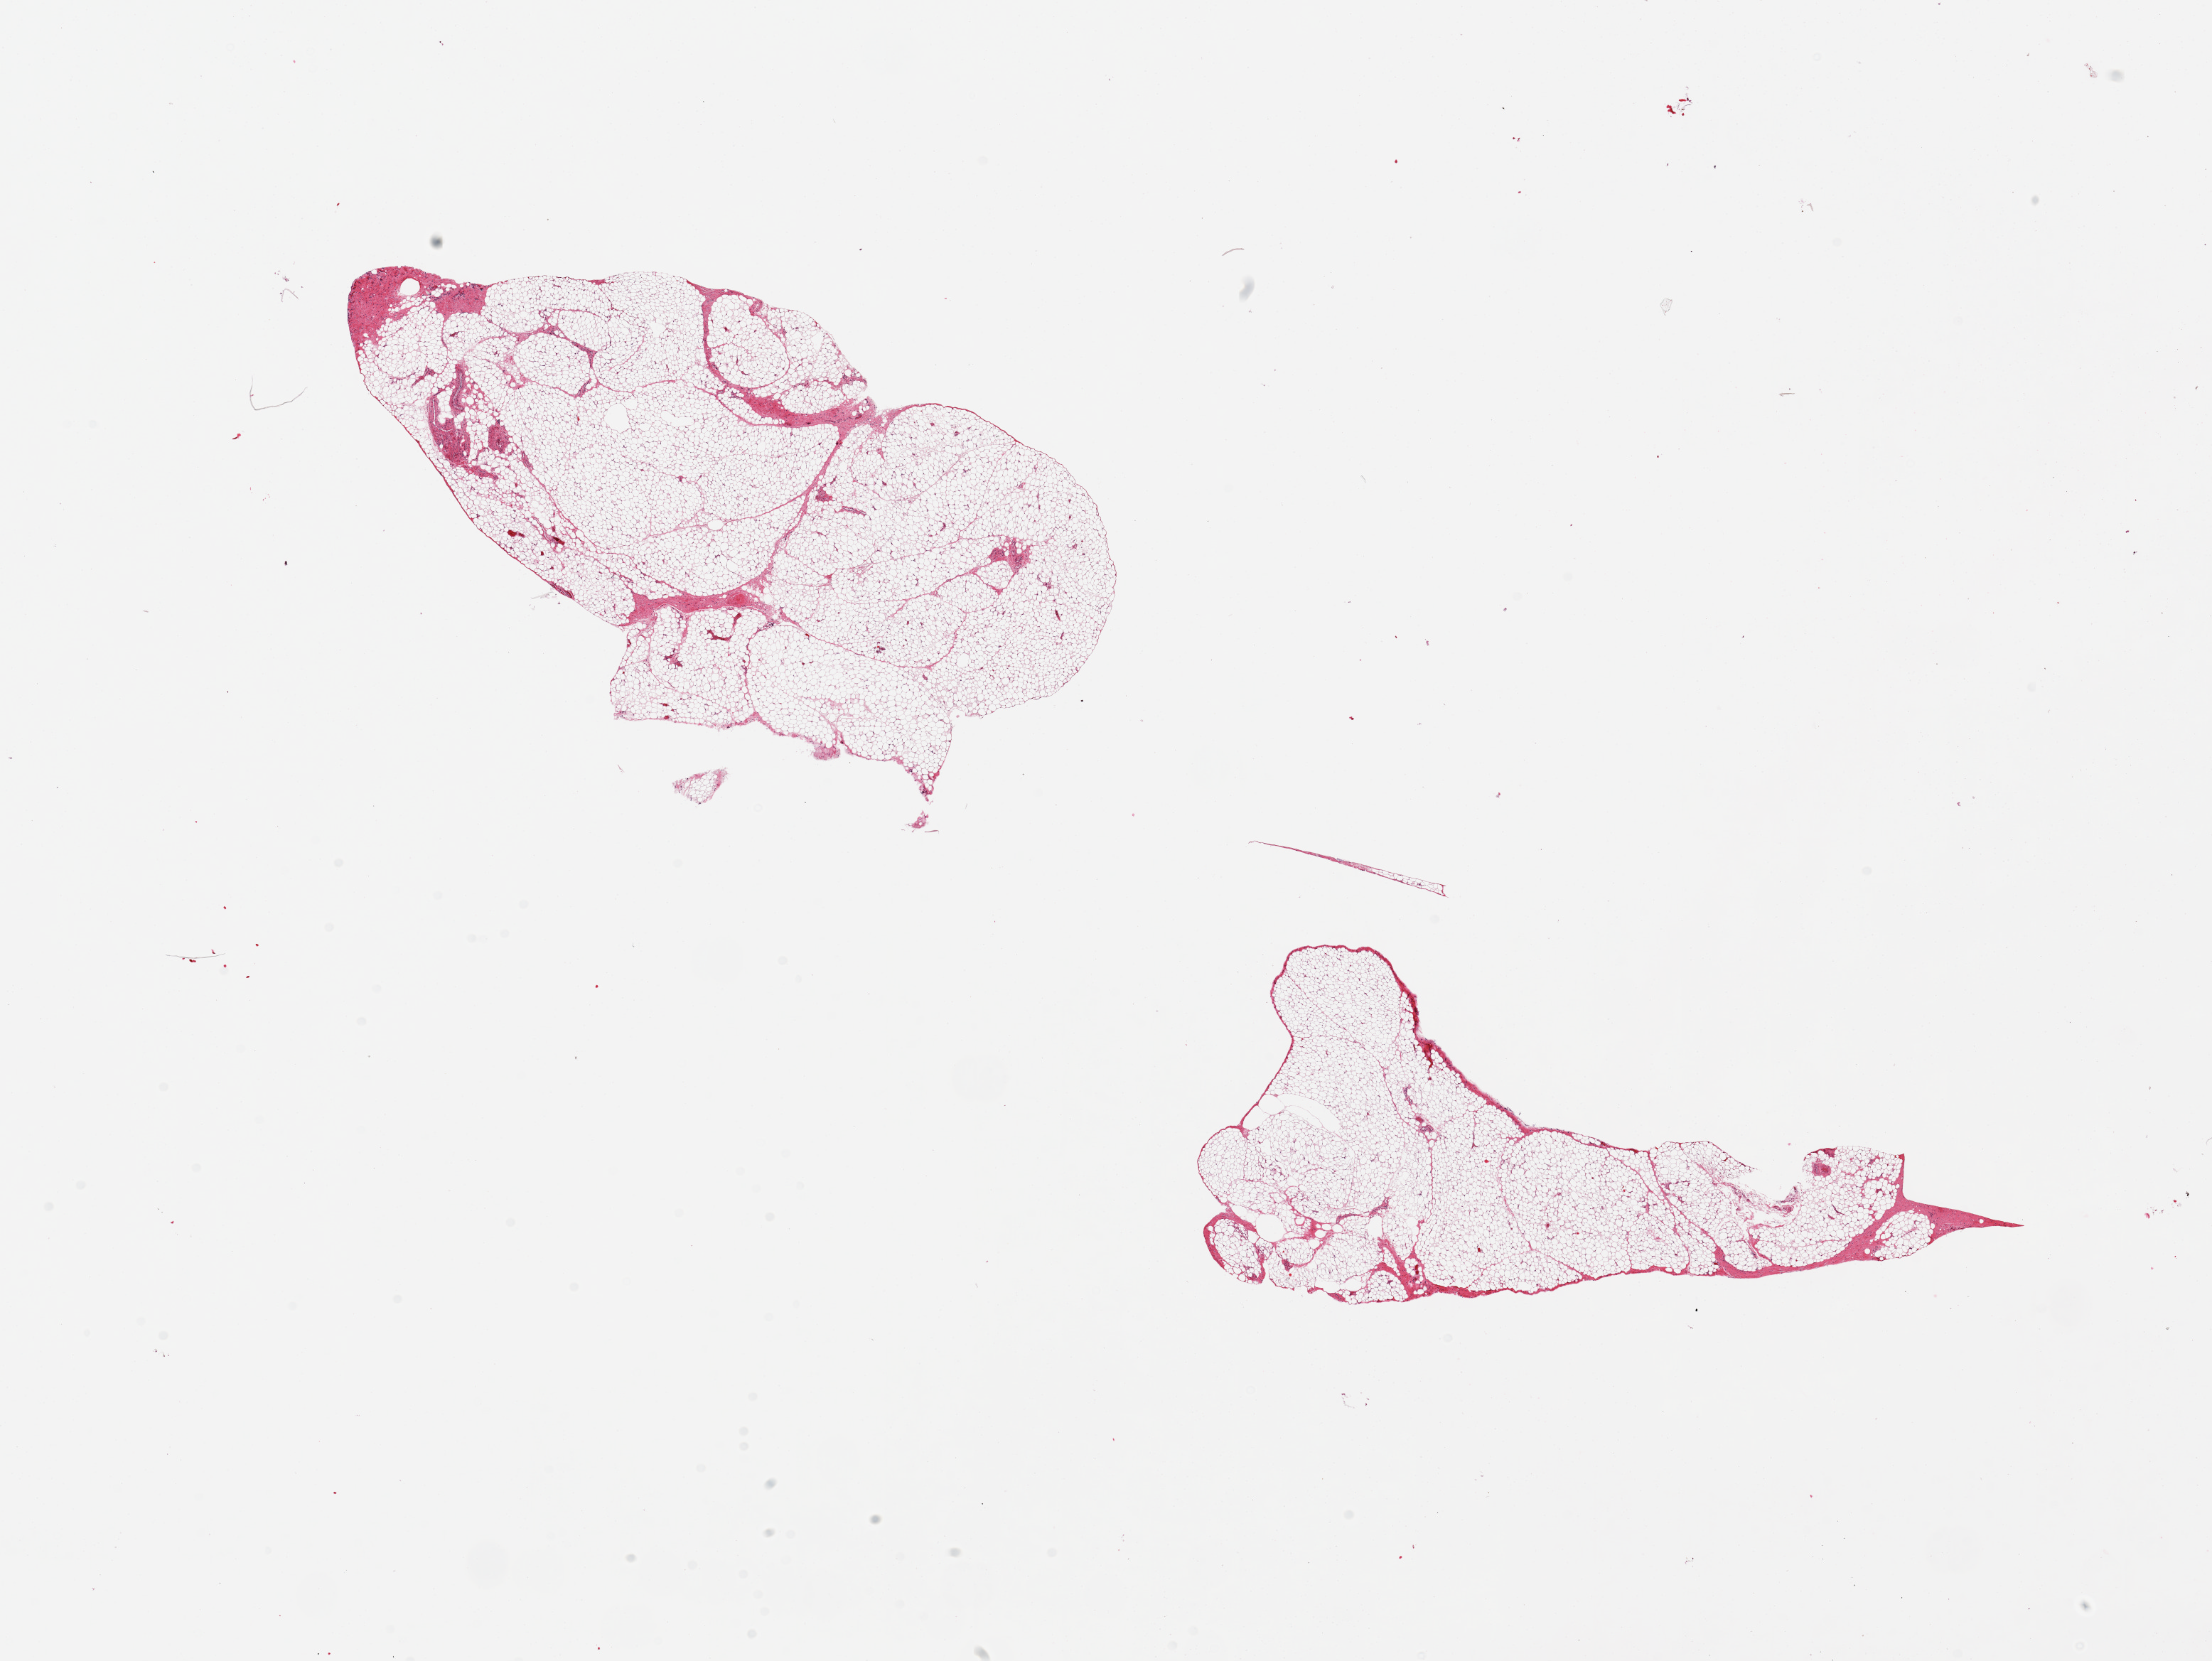
Hematoxylin and eosin (H&E) whole-slide image, brightfield, low-resolution overview of the scanned area, about 24.6 x 18.5 mm; PAXgene-fixed, paraffin-embedded tissue; target tissue: omentum; tissue donor sample. Donor sex: male.
- review note (as recorded): 2 pieces, mimimal fibrous tissue